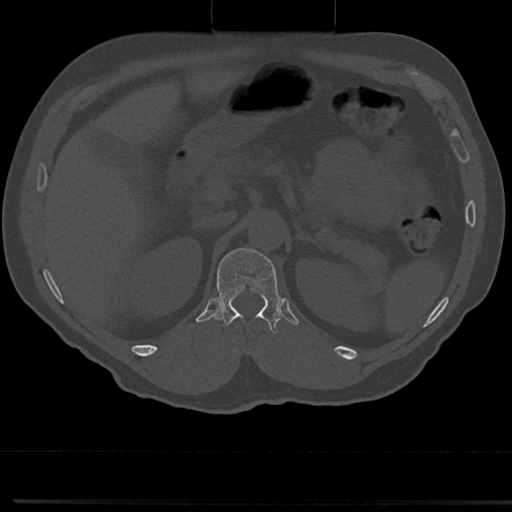
CT including the spine, one axial slice; position 147 of 817 along the scan axis; reconstruction kernel Br40s/3; bone window (W 1800 / L 400 HU); 512 × 512 image matrix, field of view 355 × 355 mm. Patient: male, 61 years. Case-level facts recorded for this patient, not image findings: primary cancer: prostate.
Outlined on this slice (semi-automatically segmented with operator editing):
- T12 vertebra: bounding box [x1, y1, x2, y2] px = [212, 245, 279, 338]